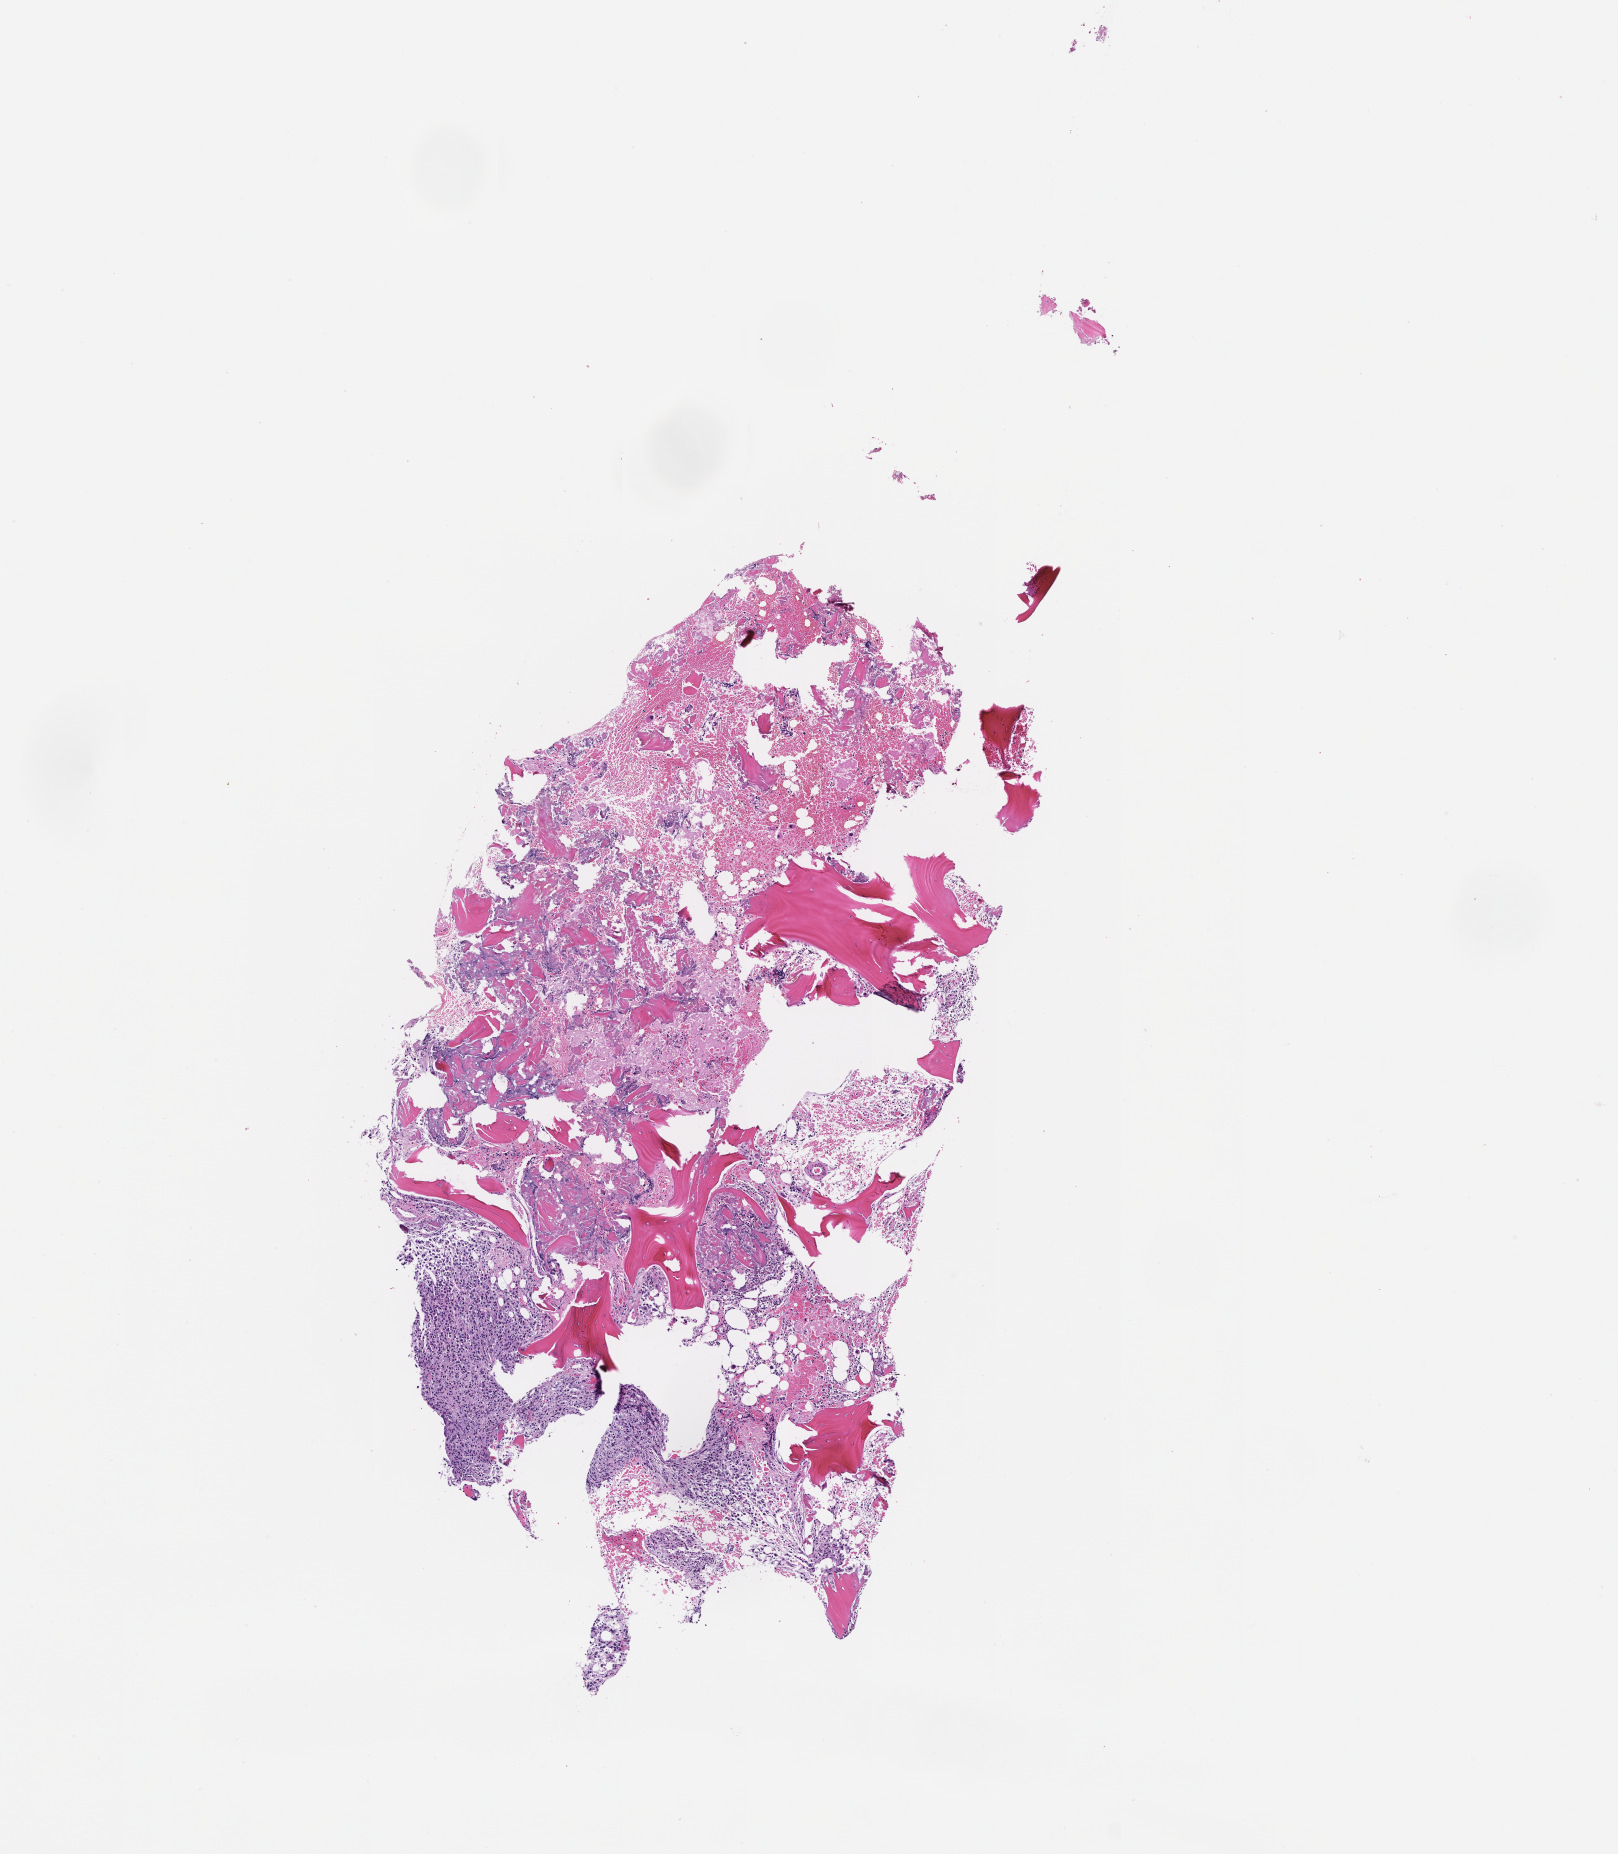
Whole-slide image, hematoxylin and eosin (H&E) stain, low-resolution overview of the scanned area, about 6.5 x 7.5 mm, formalin-fixed, paraffin-embedded (FFPE) tissue, tissue site: bone marrow, specimen time point: collected at baseline (before treatment). Female patient.
Patient diagnosis: Plasma Cell Myeloma.